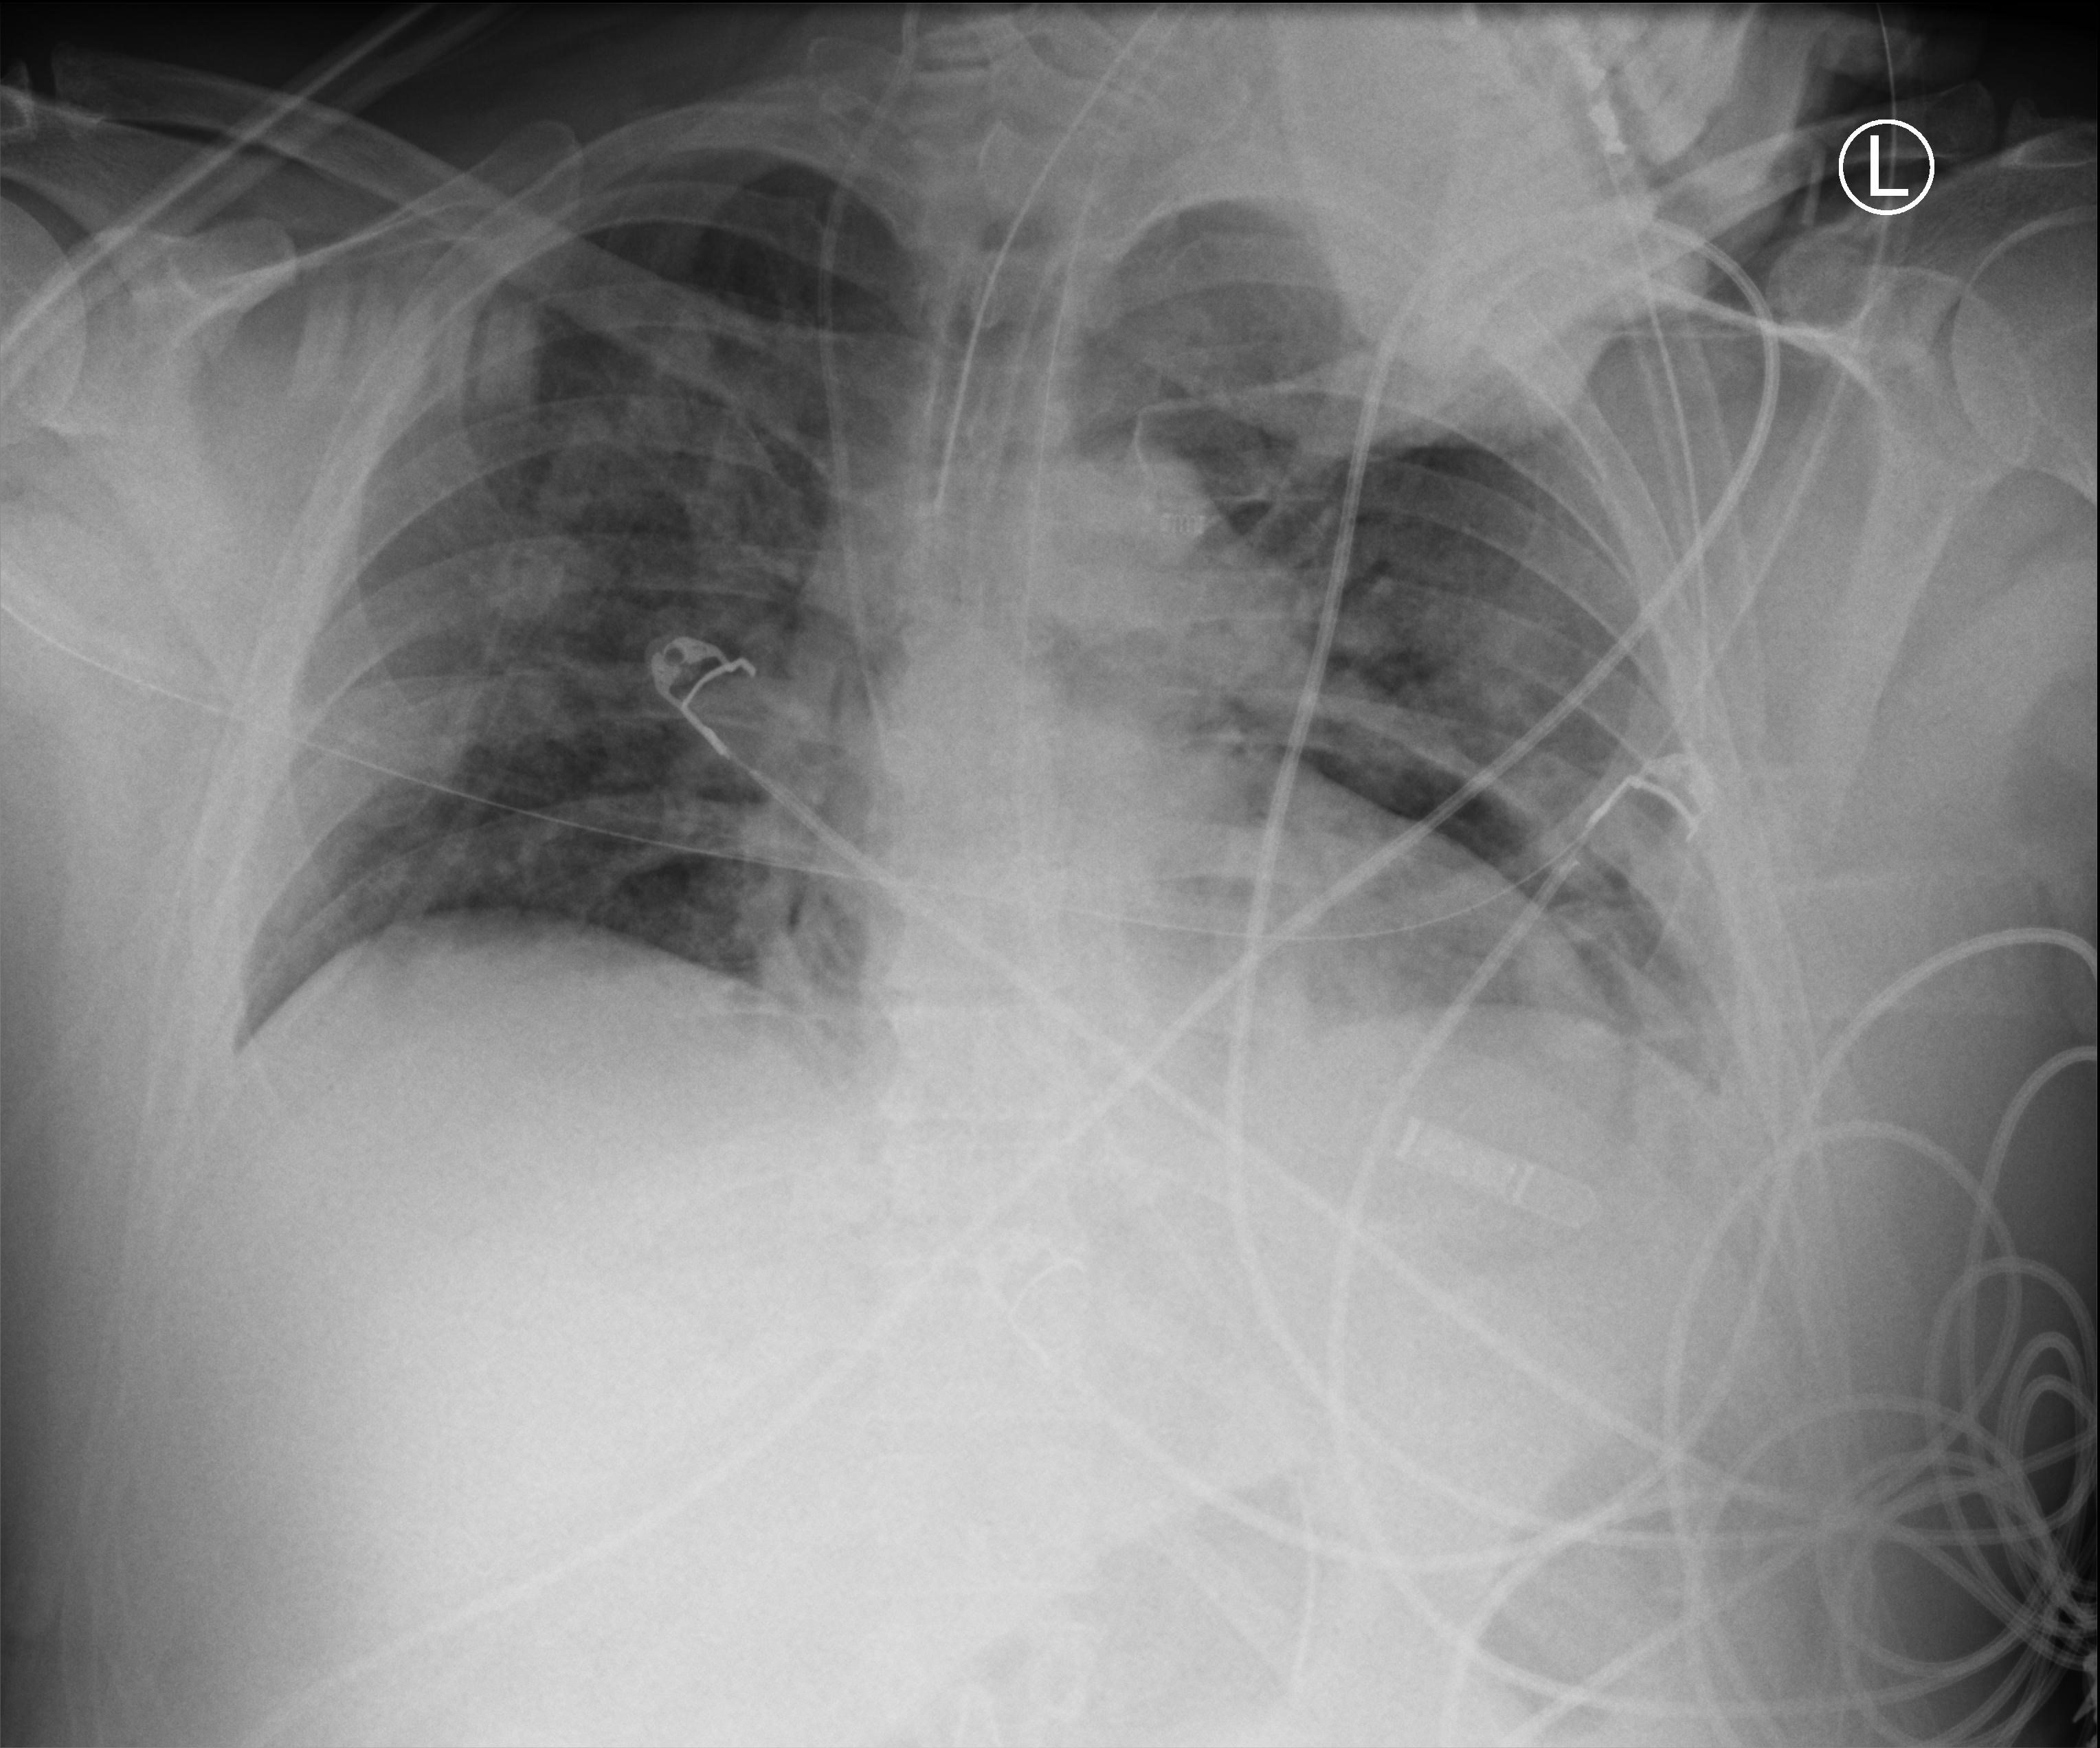
Portable chest radiograph; anteroposterior (AP) projection. Patient hospitalised with COVID-19; male, aged 18–59 years.
Admission-level facts for this patient (not findings on this image; timing relative to this image not recorded): length of hospital stay: 39 days; mechanically ventilated during this hospital stay: yes; diabetes (admission record): no.